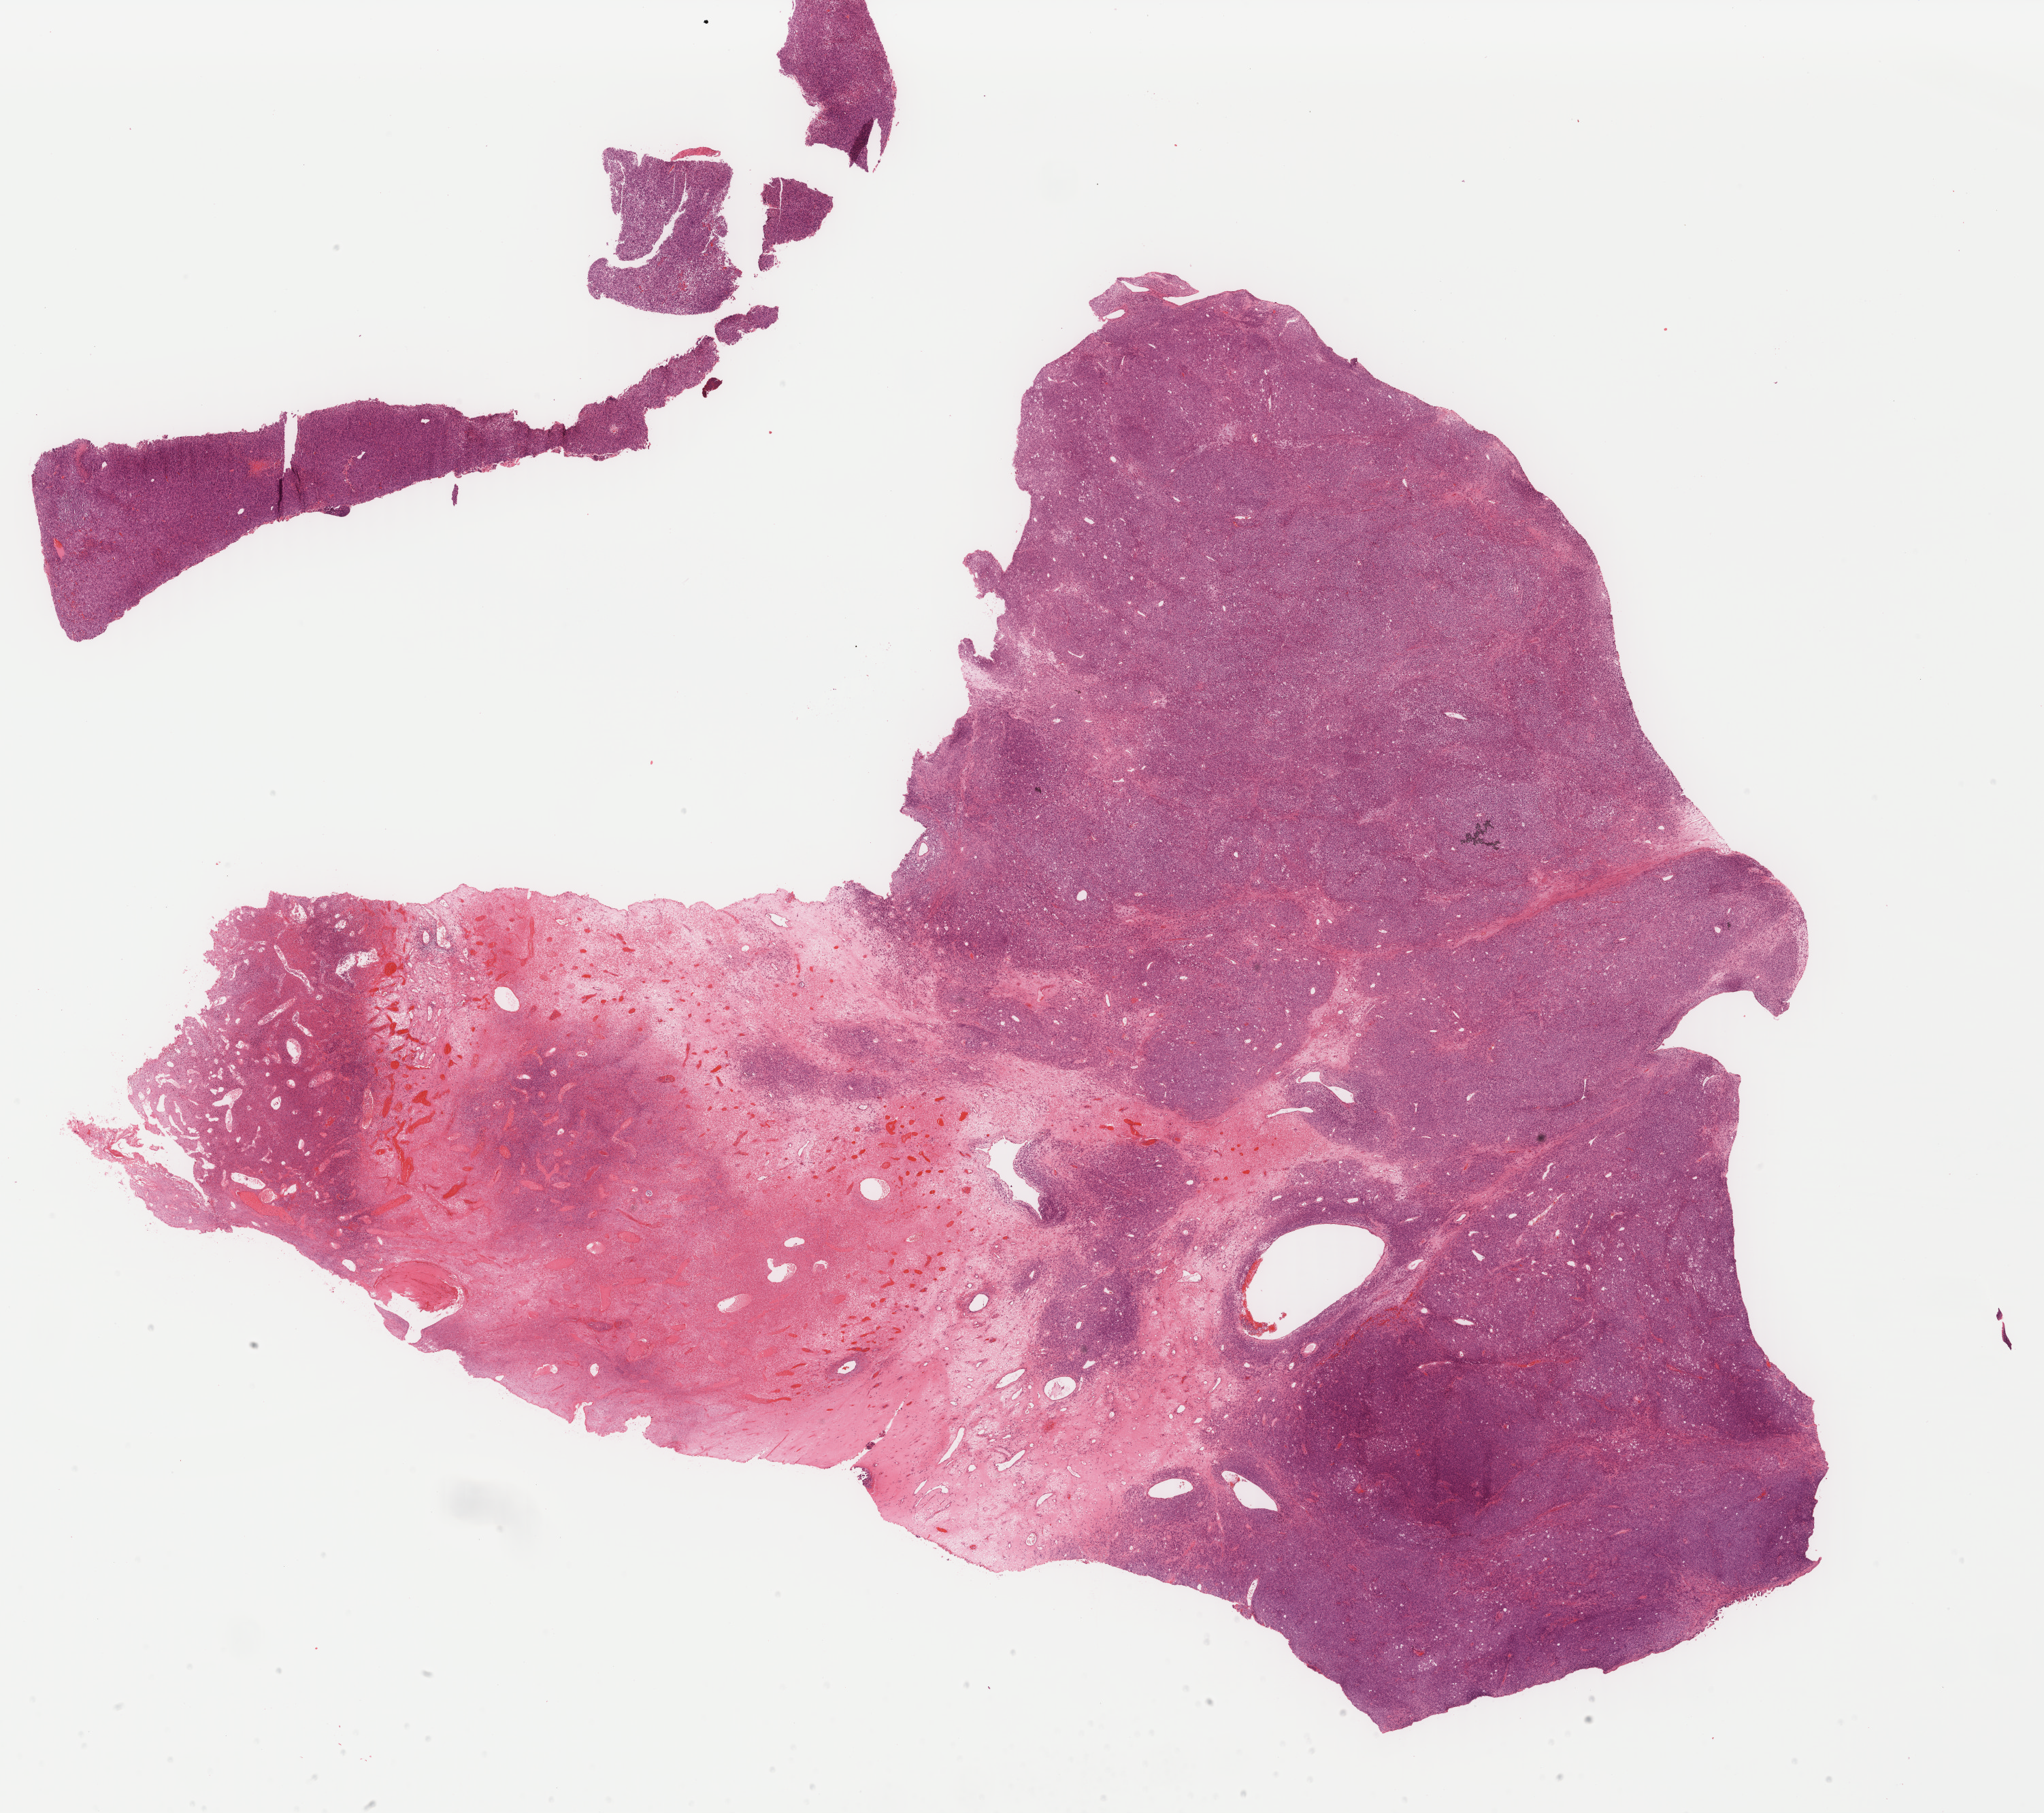
Digitized H&E tissue section (whole slide), shown as a low-resolution overview of the whole scanned area (about 23.8 x 21.2 mm, acquisition: 40x scan); FFPE section; uterus, primary tumour sample. Female patient; age at initial diagnosis 72 years.
• FIGO stage: IVB
• diagnosis: Mullerian mixed tumor